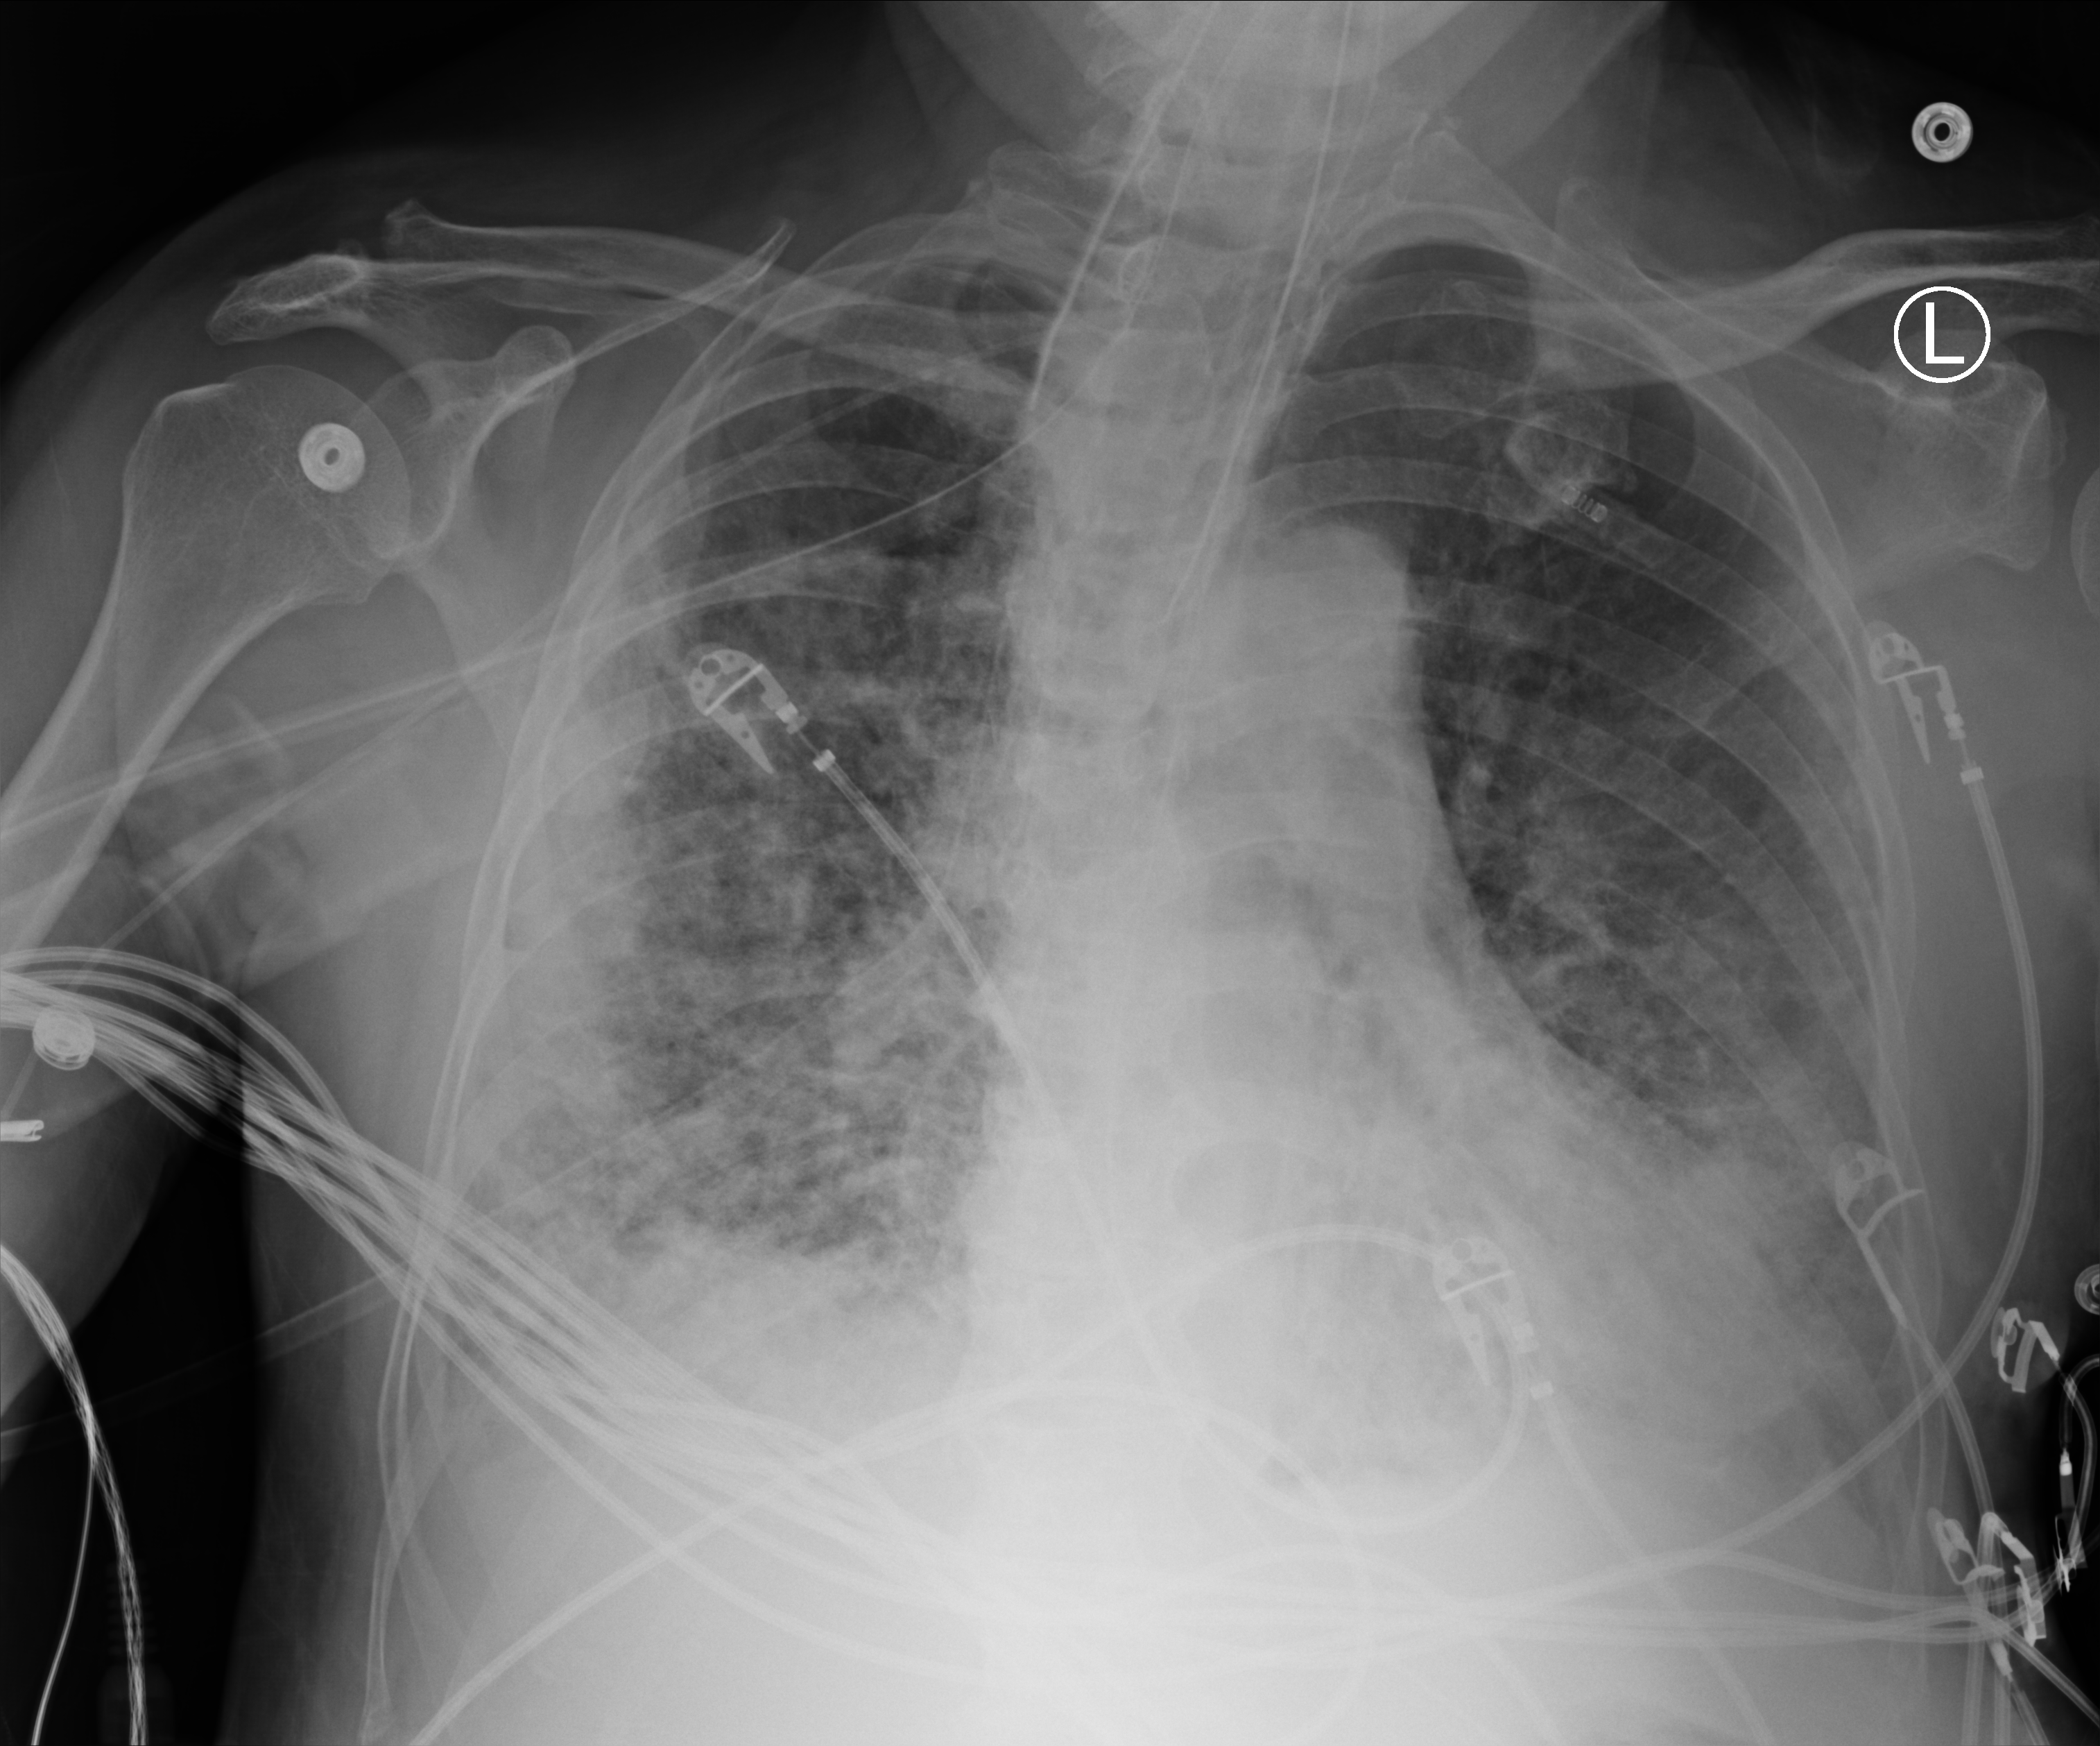
Chest X-ray (portable), anteroposterior (AP) projection. Male patient hospitalised with COVID-19, age 60–74 years.
From the hospital-stay record, not from the radiograph (when in the stay this image was taken is not recorded): admitted to intensive care during this hospital stay: yes.